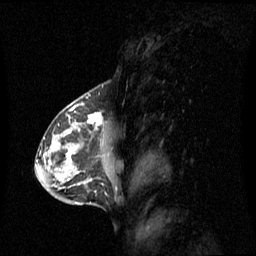
Breast MRI (dynamic contrast-enhanced), one sagittal slice; position 38 of 60 along the scan axis; dynamic contrast-enhanced series, image 2 of 3 at this slice position (ordered by acquisition); 1.5 T; TE 4.2 ms, TR 8.4 ms; 2 mm slice thickness; 256 × 256 image matrix, field of view 270 × 270 mm. Female patient, age 42 years. From the clinical record (not read from this slice): setting: breast cancer imaged before/during neoadjuvant chemotherapy; receptor status: HR-positive, HER2-negative.
Structures marked on this image (semi-automatically segmented with operator editing):
- analysis volume of interest (the breast-tissue region the enhancement analysis was run in; not a lesion): bounding box <56,112,120,185> (left, top, right, bottom; pixels)
- tumour enhancement mask (voxels above the 70 % enhancement threshold inside the analysis volume of interest): <66,113,102,162>